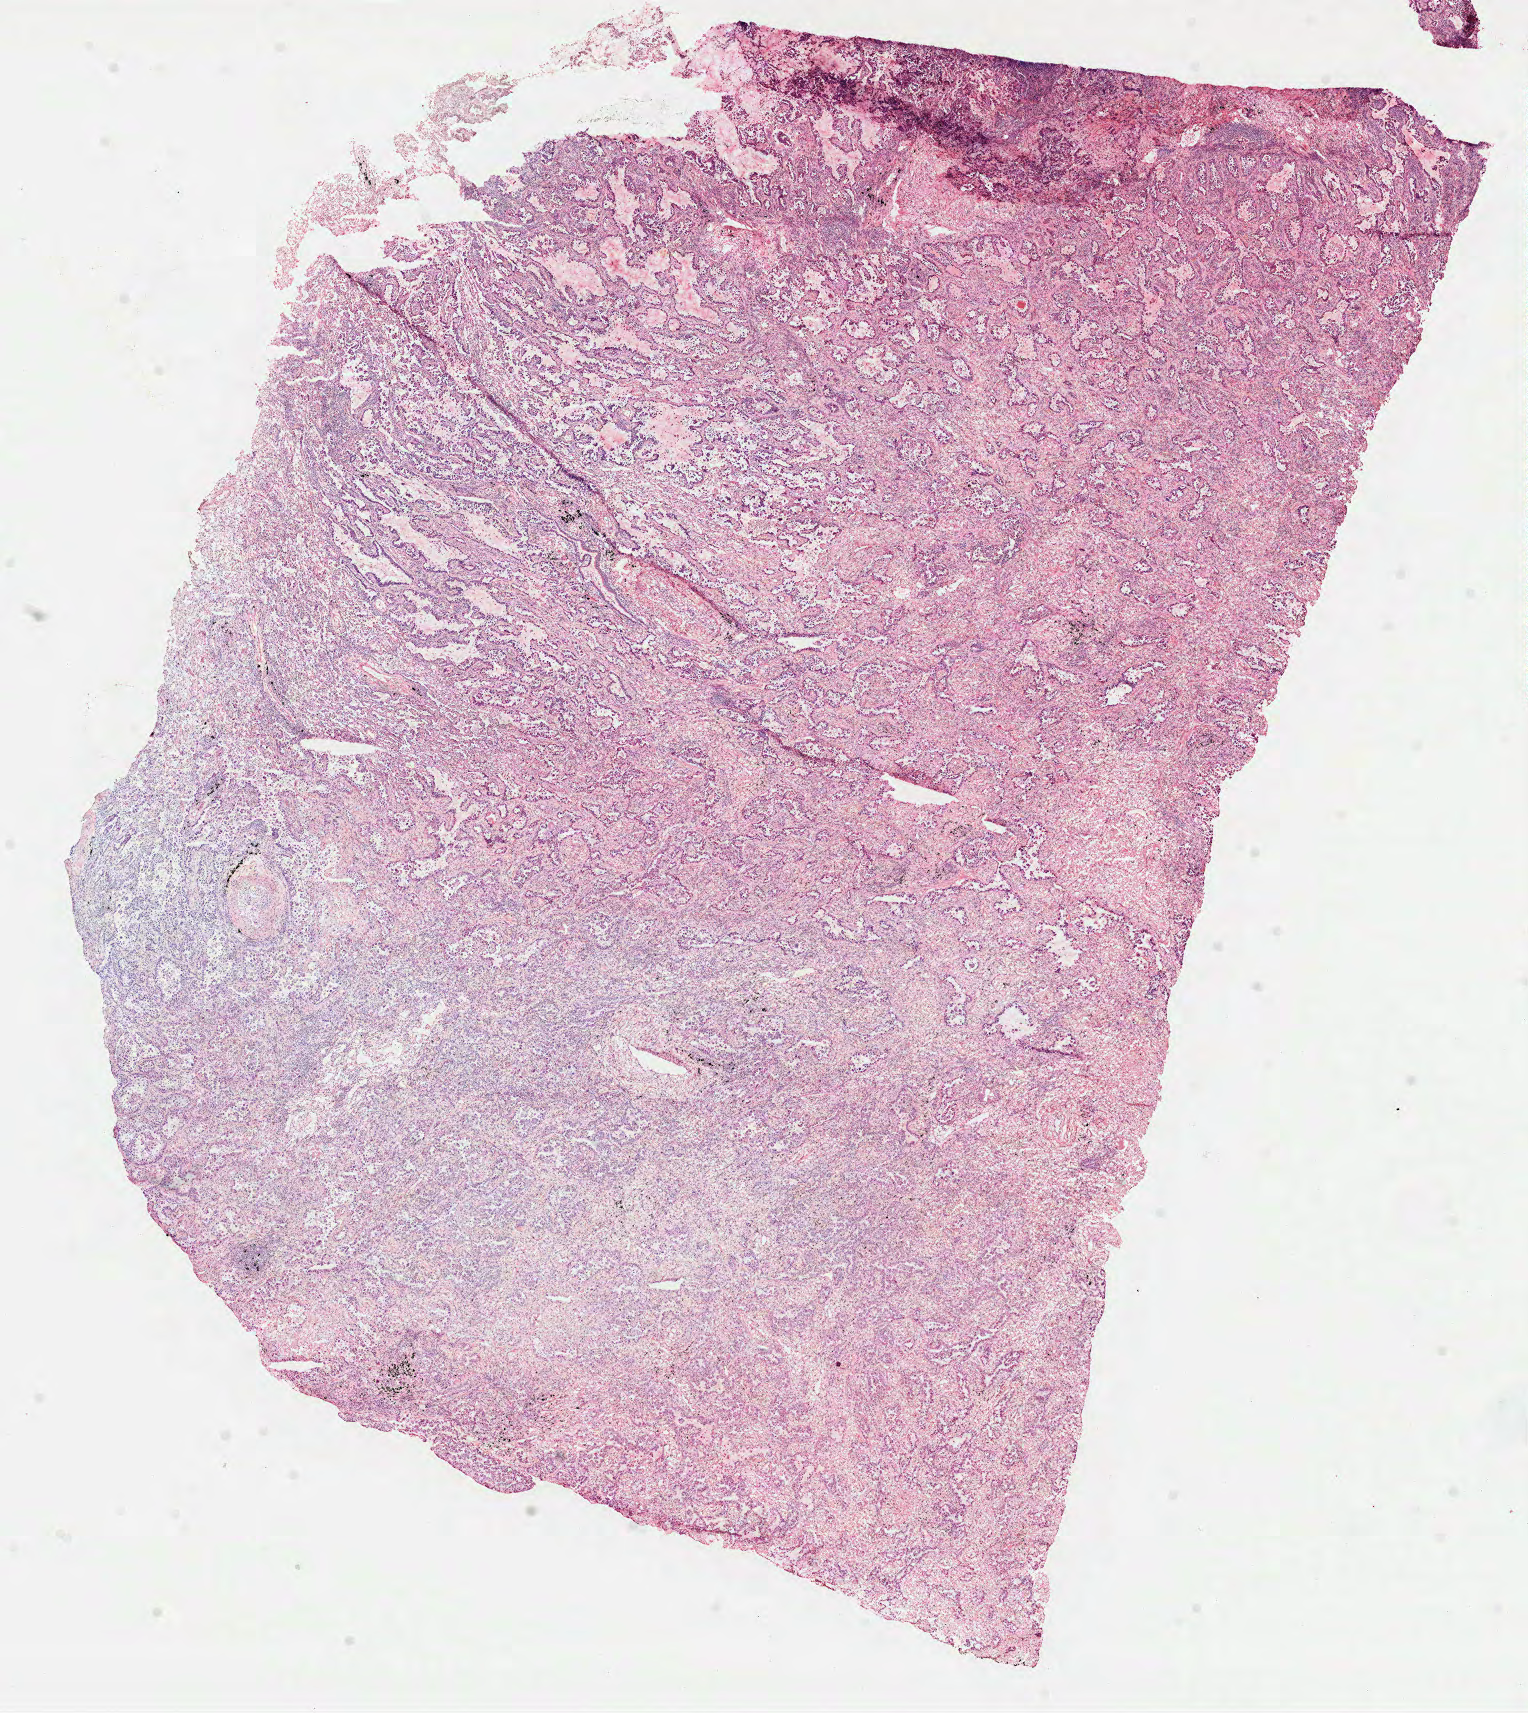
Hematoxylin and eosin (H&E) stained whole-slide image, shown as a low-resolution overview of the whole scanned area (about 12.3 x 13.8 mm, acquisition: 40x scan); frozen section from the top of the tissue portion; lung, primary tumour sample. Female patient; age at initial diagnosis 83 years. Composition of this section per pathologist review: tumour cells 100%, tumour nuclei 65%, necrosis 0%. Inflammatory infiltration, as recorded: lymphocyte infiltration 10%, monocyte infiltration 2%.
* diagnosis: Papillary adenocarcinoma, NOS (lower lobe, lung)
* AJCC pathologic stage: IIIA (7th edition)